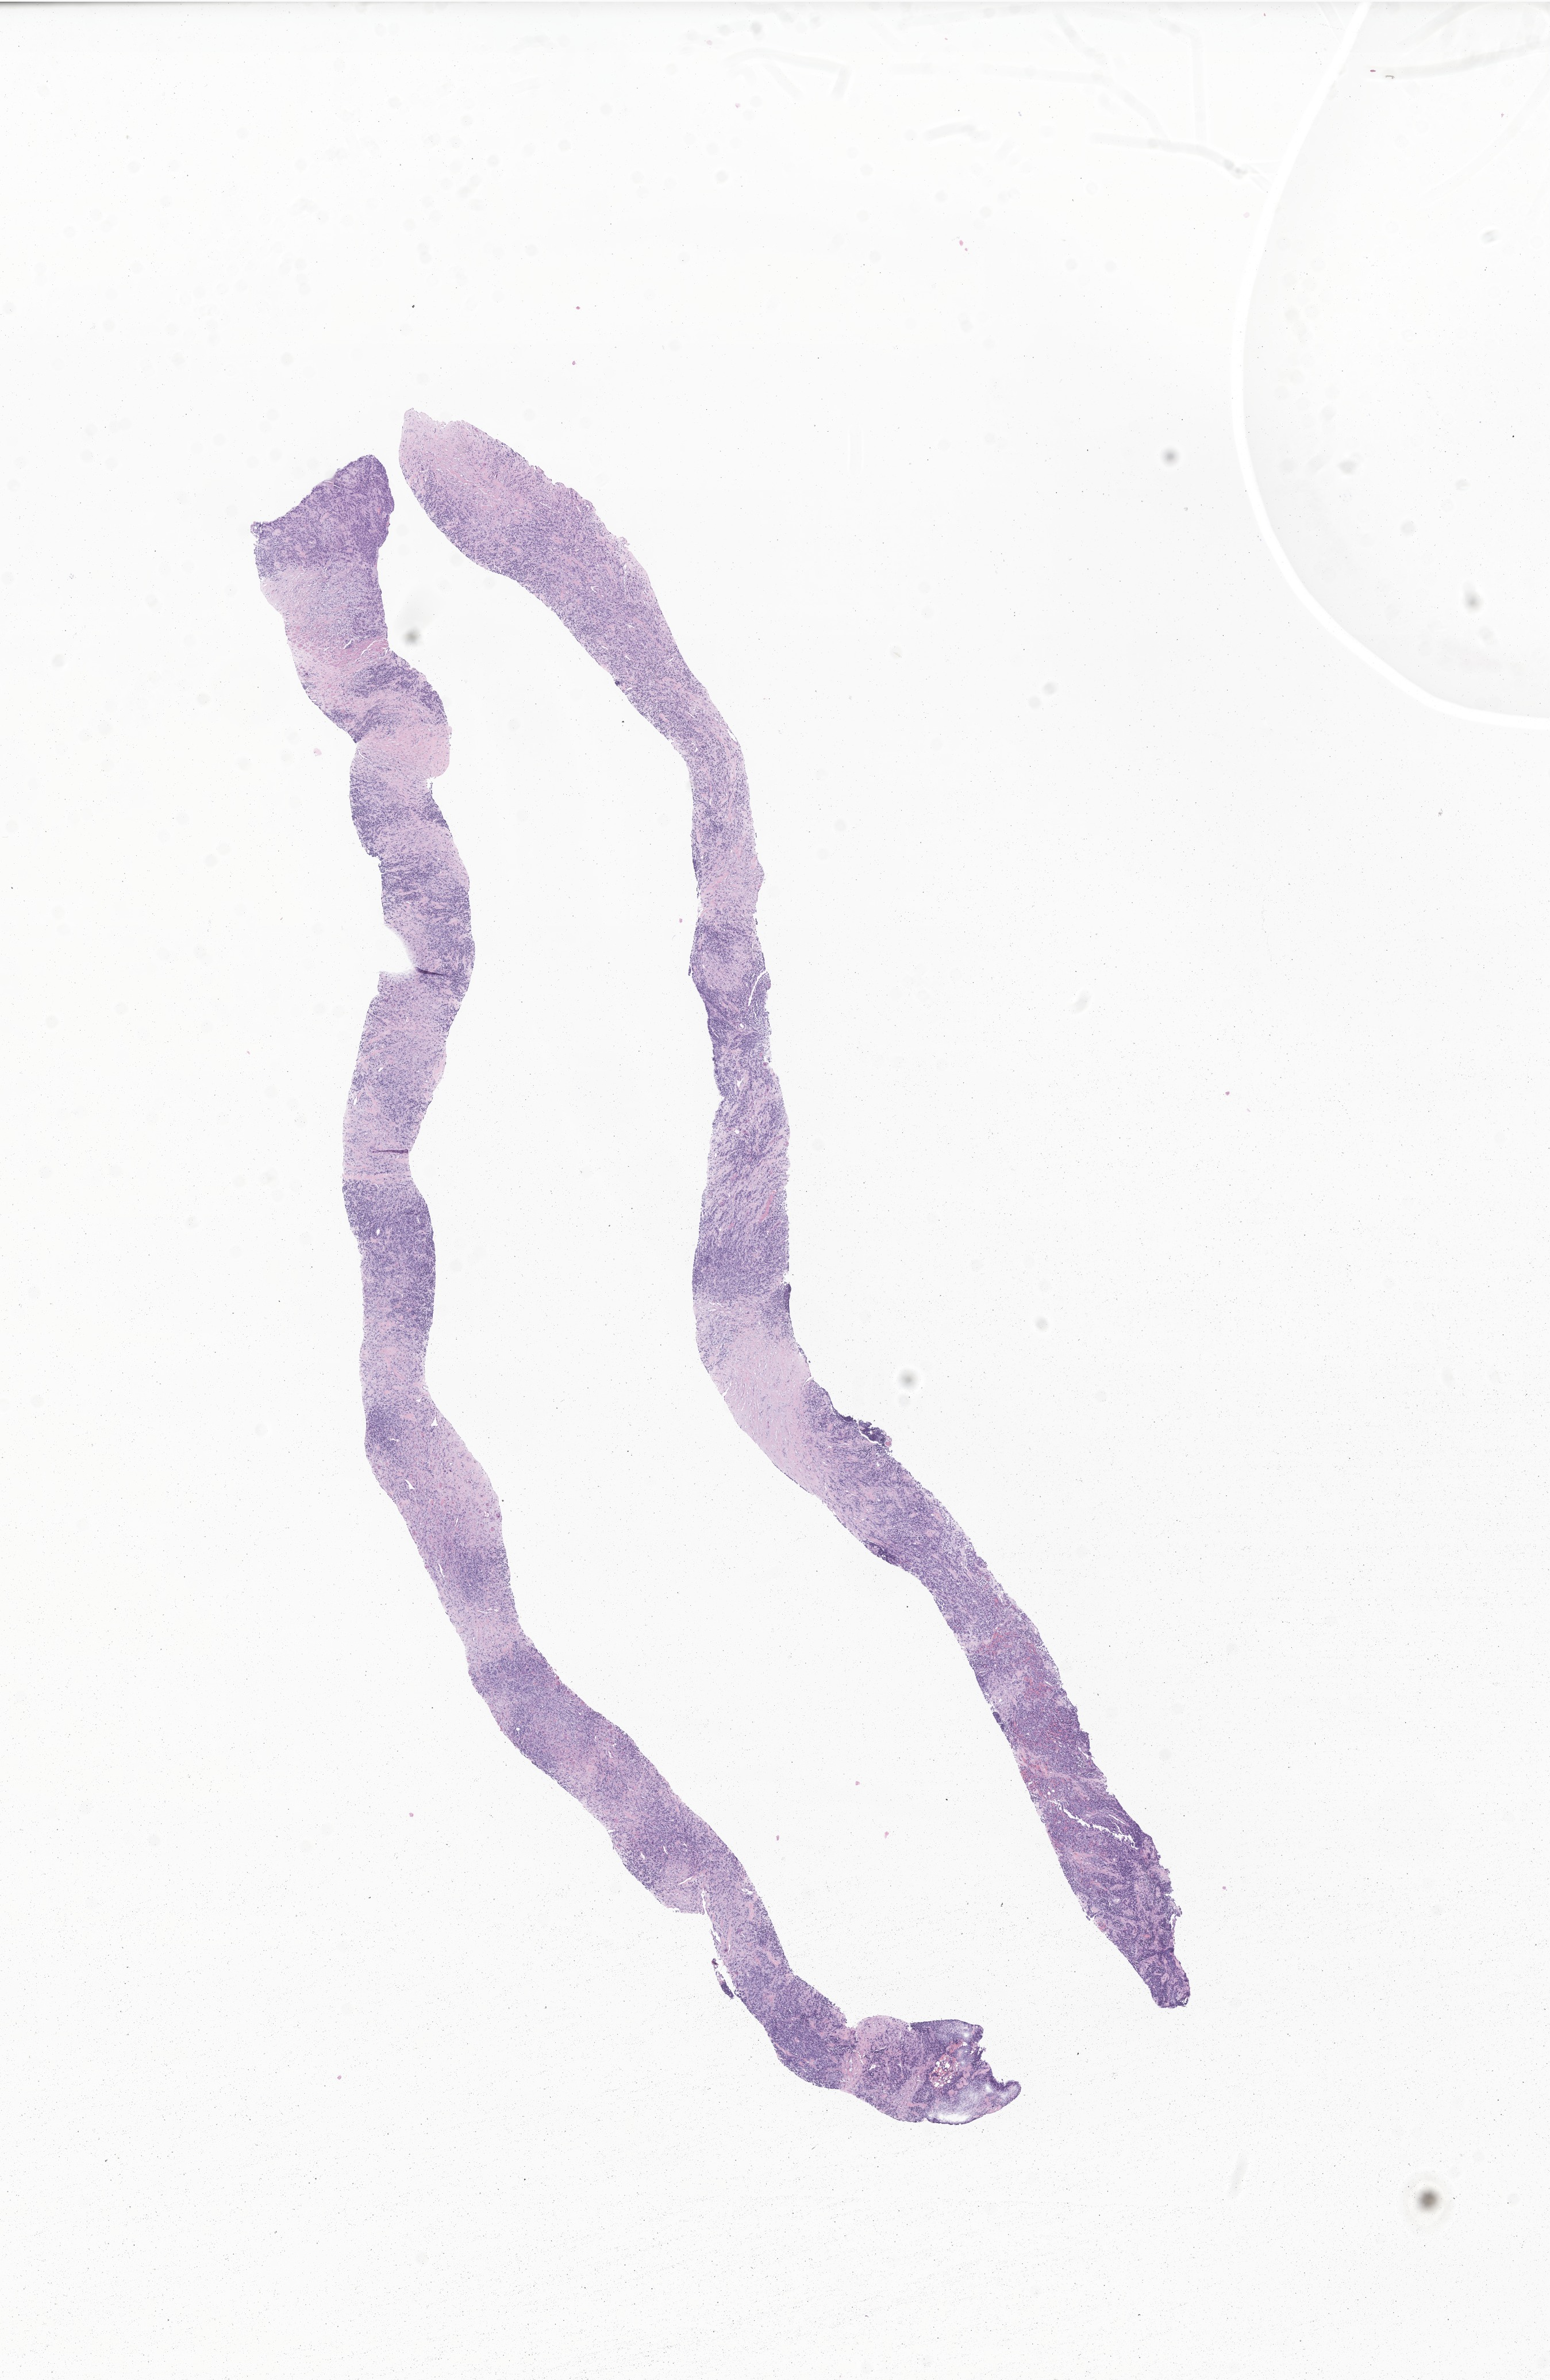
Hematoxylin and eosin (H&E) whole-slide image of tumor tissue from the soft tissue of lower extremity, shown as a low-resolution overview of the whole scanned area (about 11.4 x 17.5 mm), FFPE section. Patient male; age 98 months (8 years 2 months).
• diagnosis (ICD-O-3 morphology term): Alveolar rhabdomyosarcoma